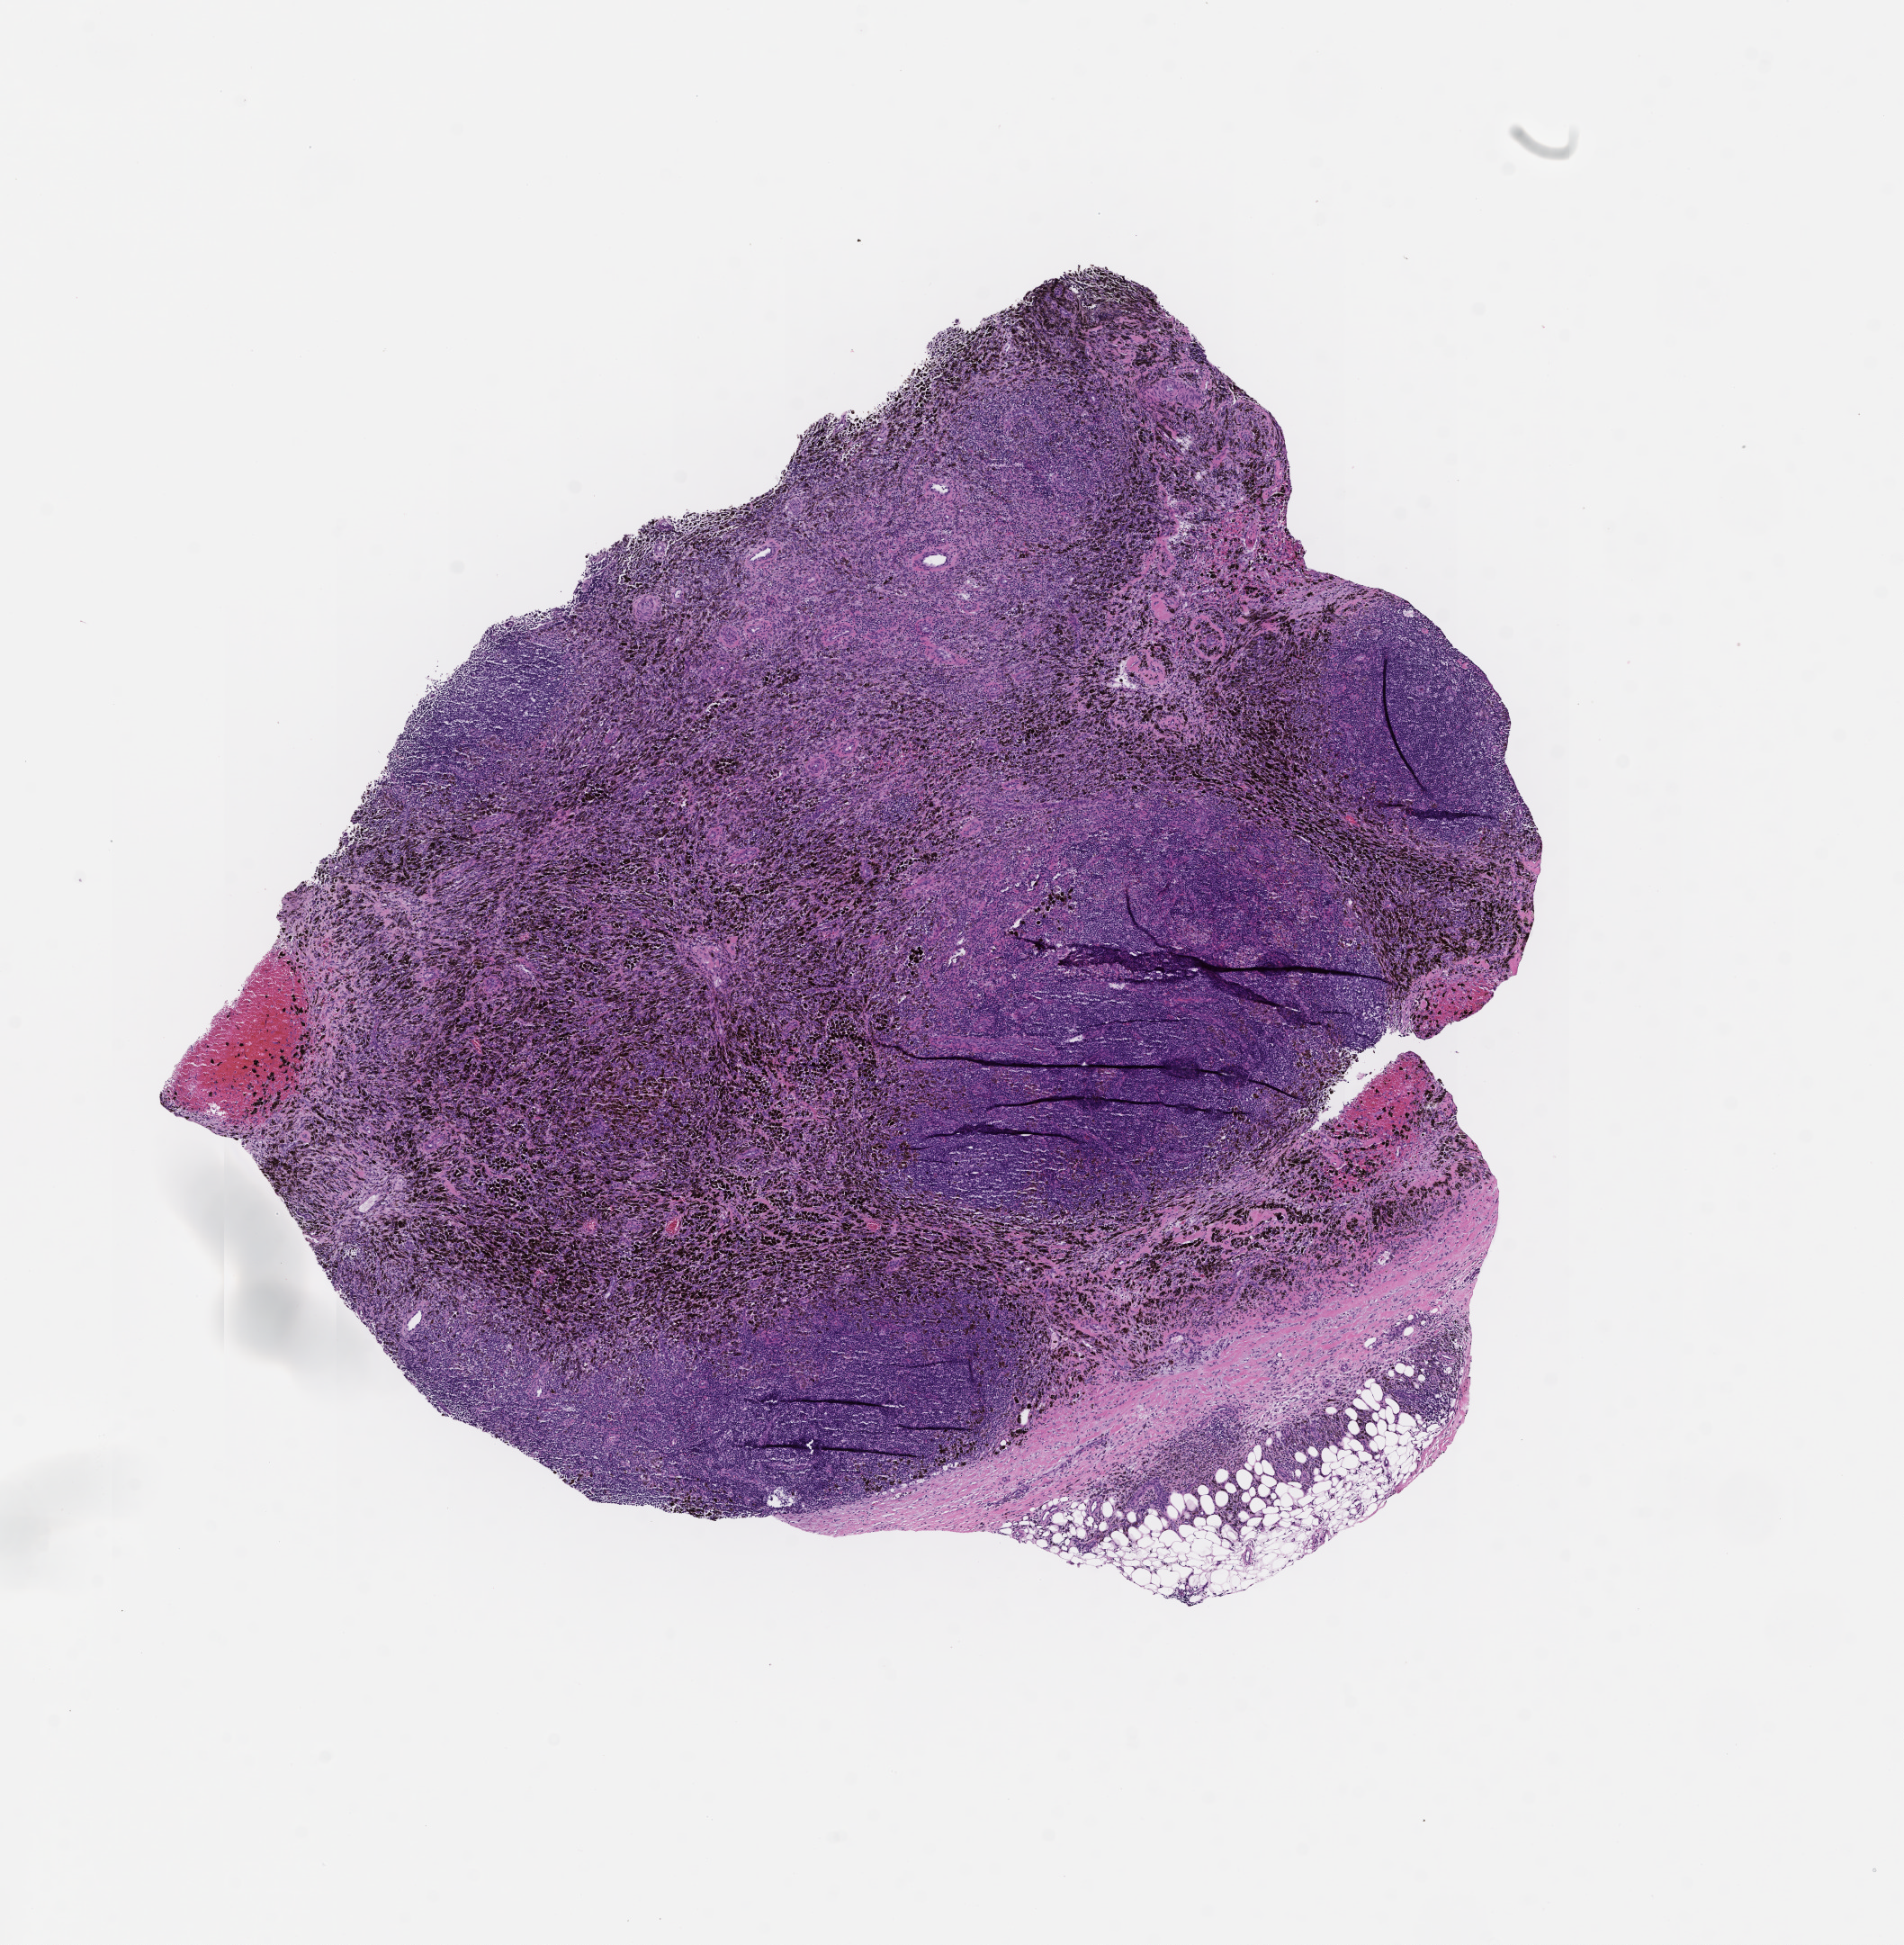
Hematoxylin and eosin (H&E) whole-slide image — whole scanned area (about 8.5 x 8.7 mm) shown as a low-resolution overview. FFPE section. Tissue site: skin. Male patient.
- this section: primary tumour tissue
- diagnosis: Melanoma